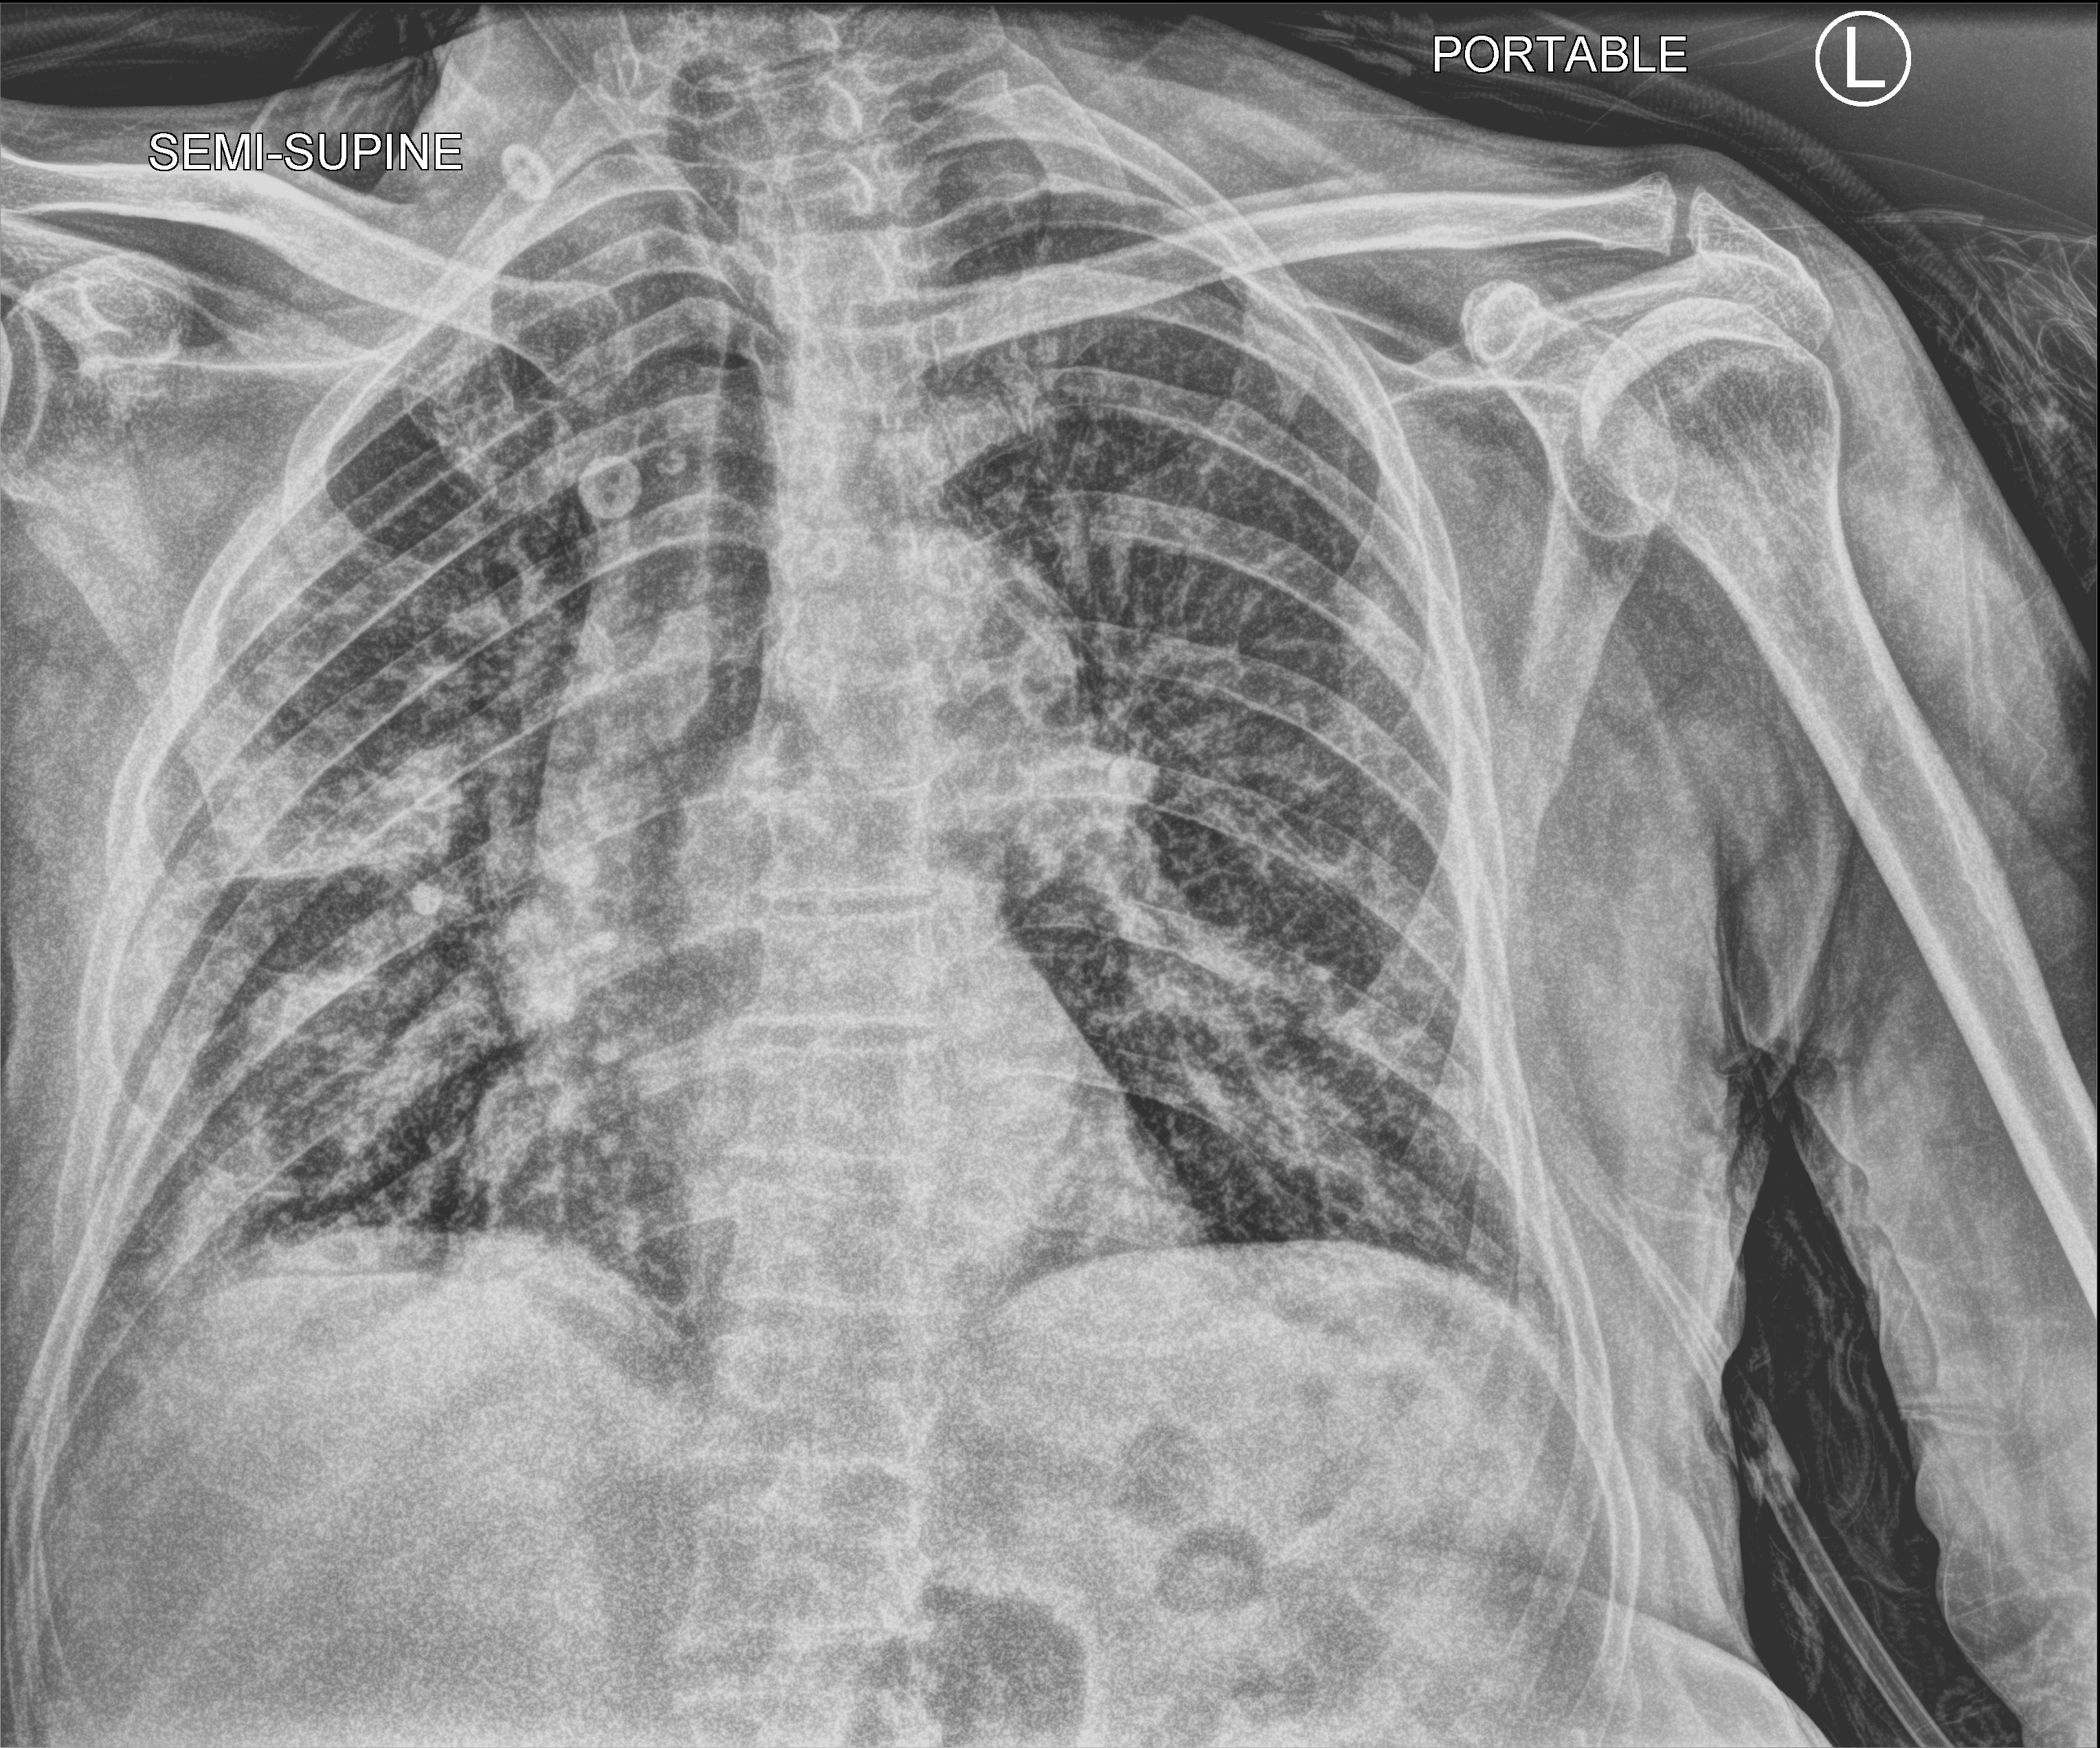
Portable chest radiograph. Patient hospitalised with COVID-19; male, aged 75–90 years.
Admission-level facts for this patient (not findings on this image; timing relative to this image not recorded):
- mechanically ventilated during this hospital stay: yes
- smoking status (admission record): never